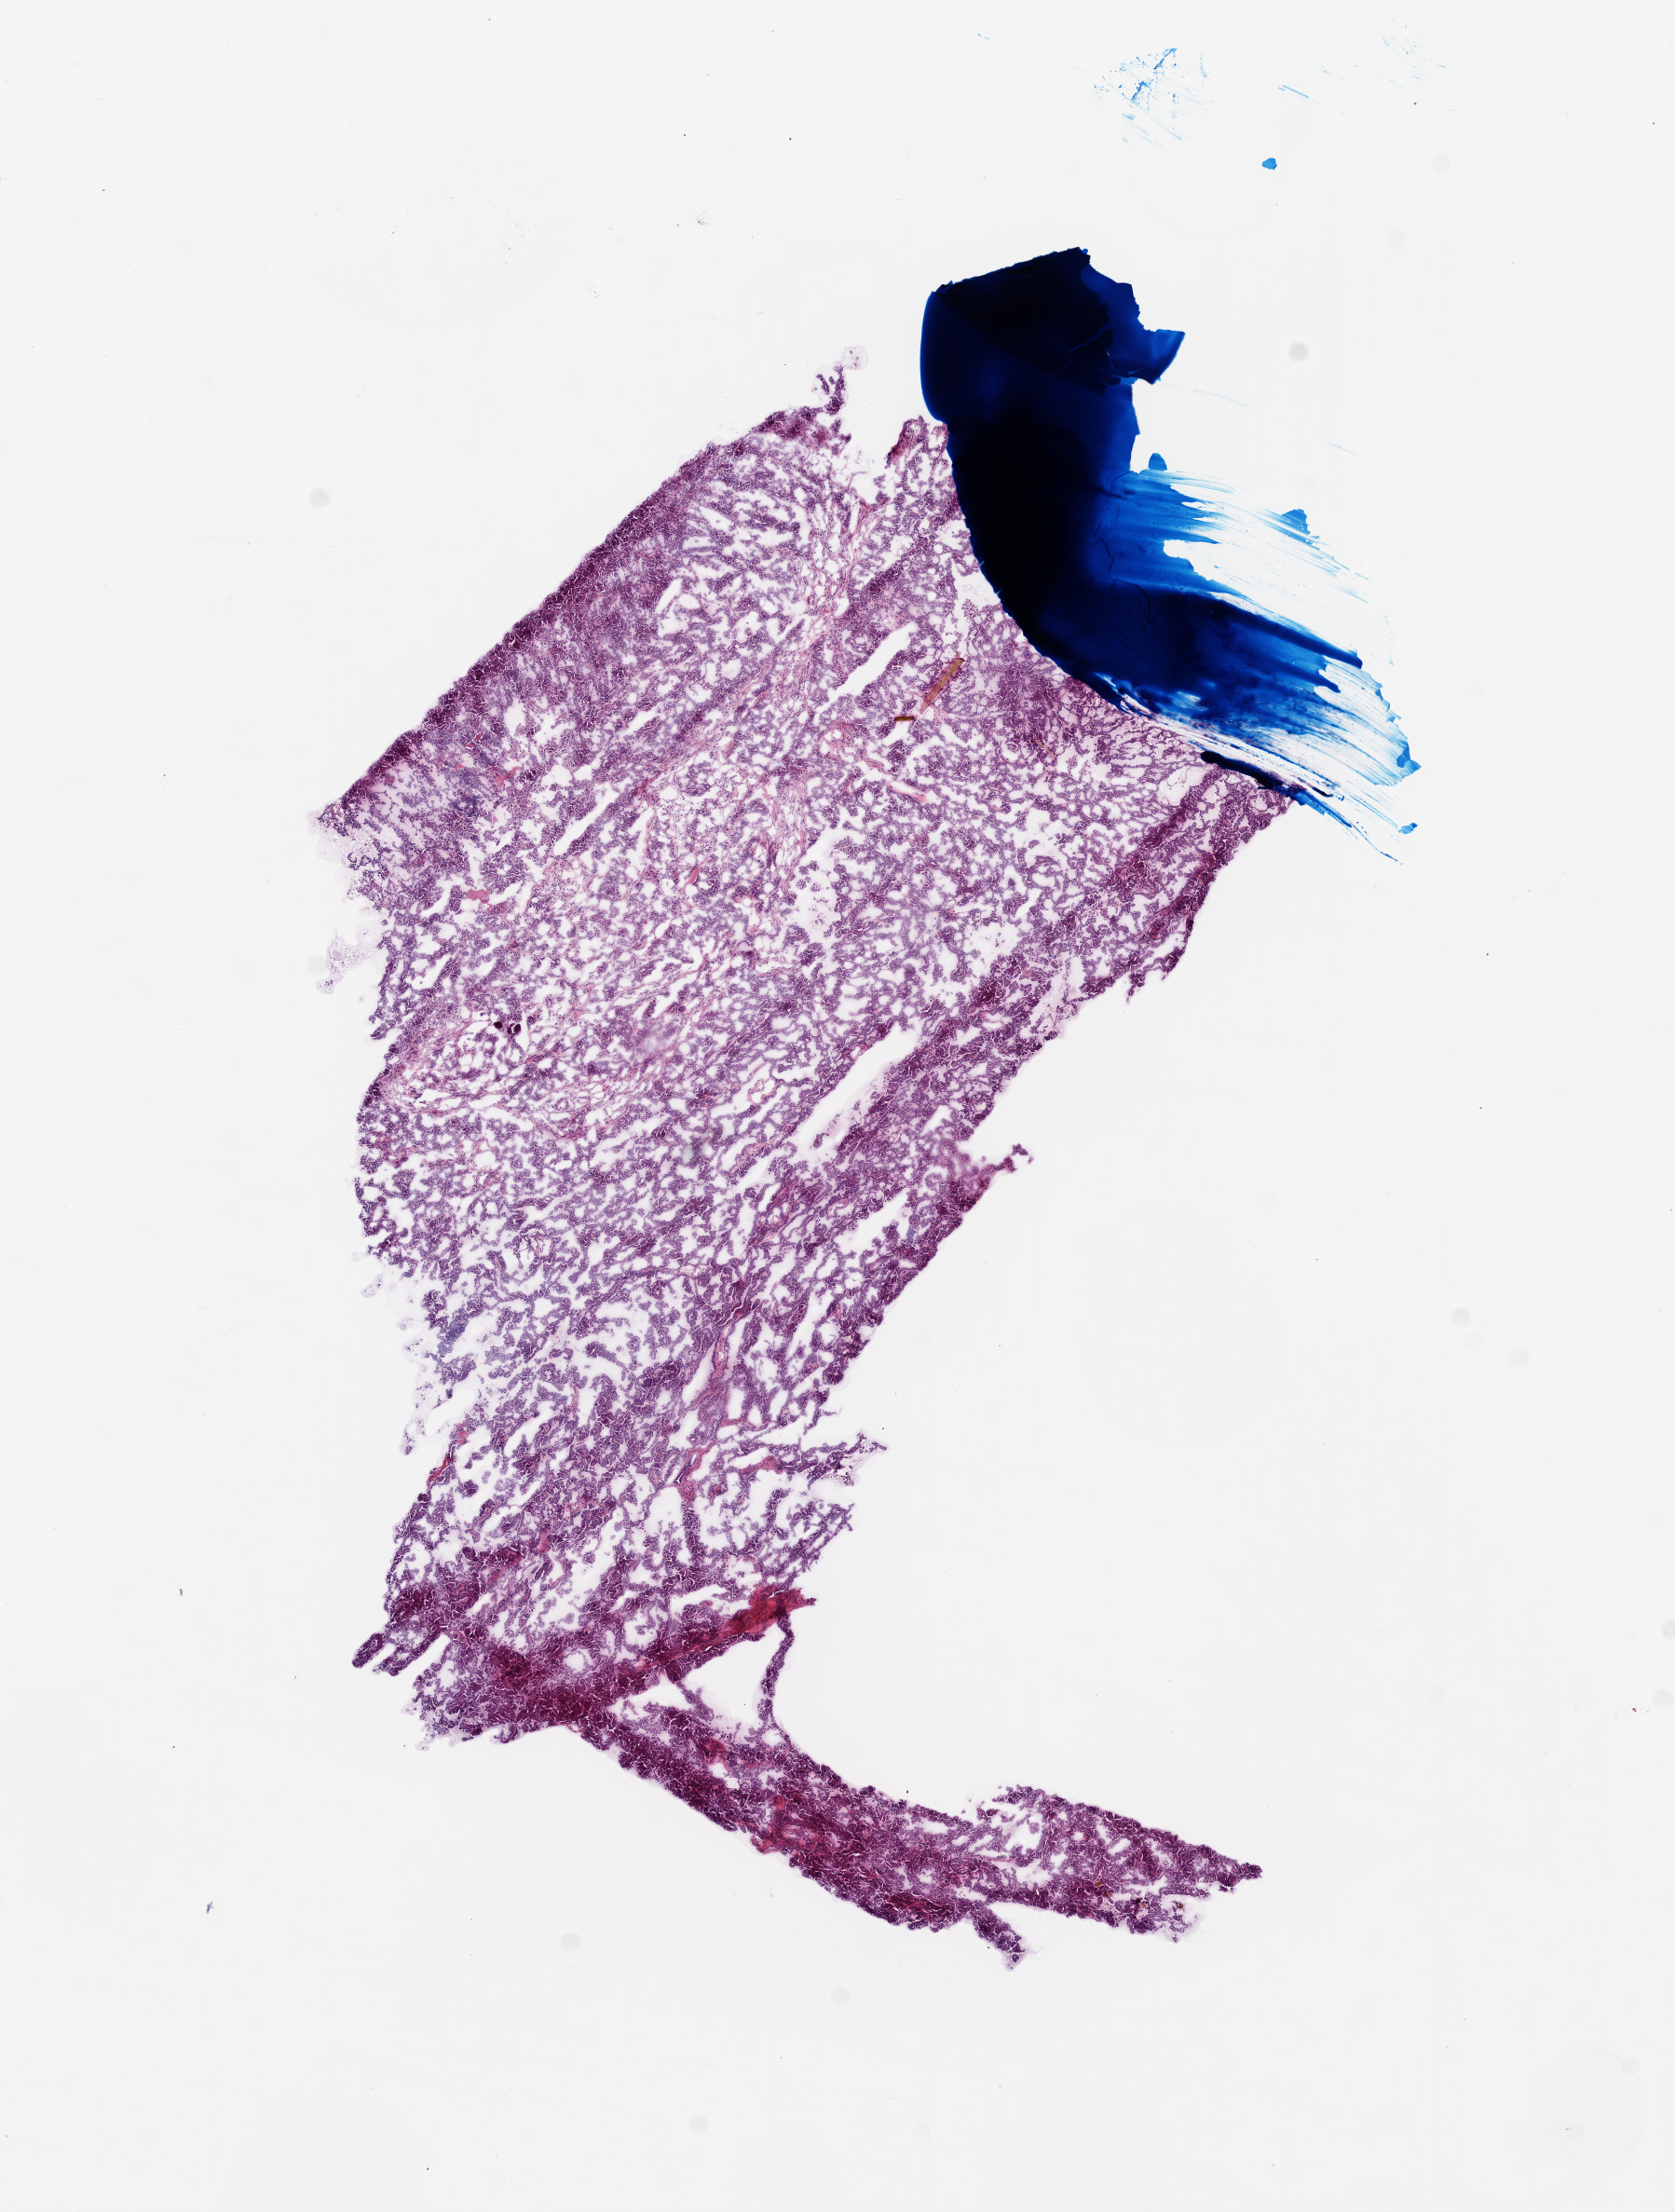
Hematoxylin and eosin (H&E) stained whole-slide image, low-resolution overview of the scanned area, about 7.3 x 9.6 mm; frozen section; primary tumour sample from the ovary. Female patient; age at initial diagnosis 44 years. Histologic grade: G3 (poorly differentiated). Composition of this section per pathologist review: tumour cells 85%, tumour nuclei 85%, normal cells 5%, stromal cells 10%, necrosis 0%.
Pathologic diagnosis: Serous cystadenocarcinoma, NOS. Laterality: bilateral. FIGO stage: IIIC.